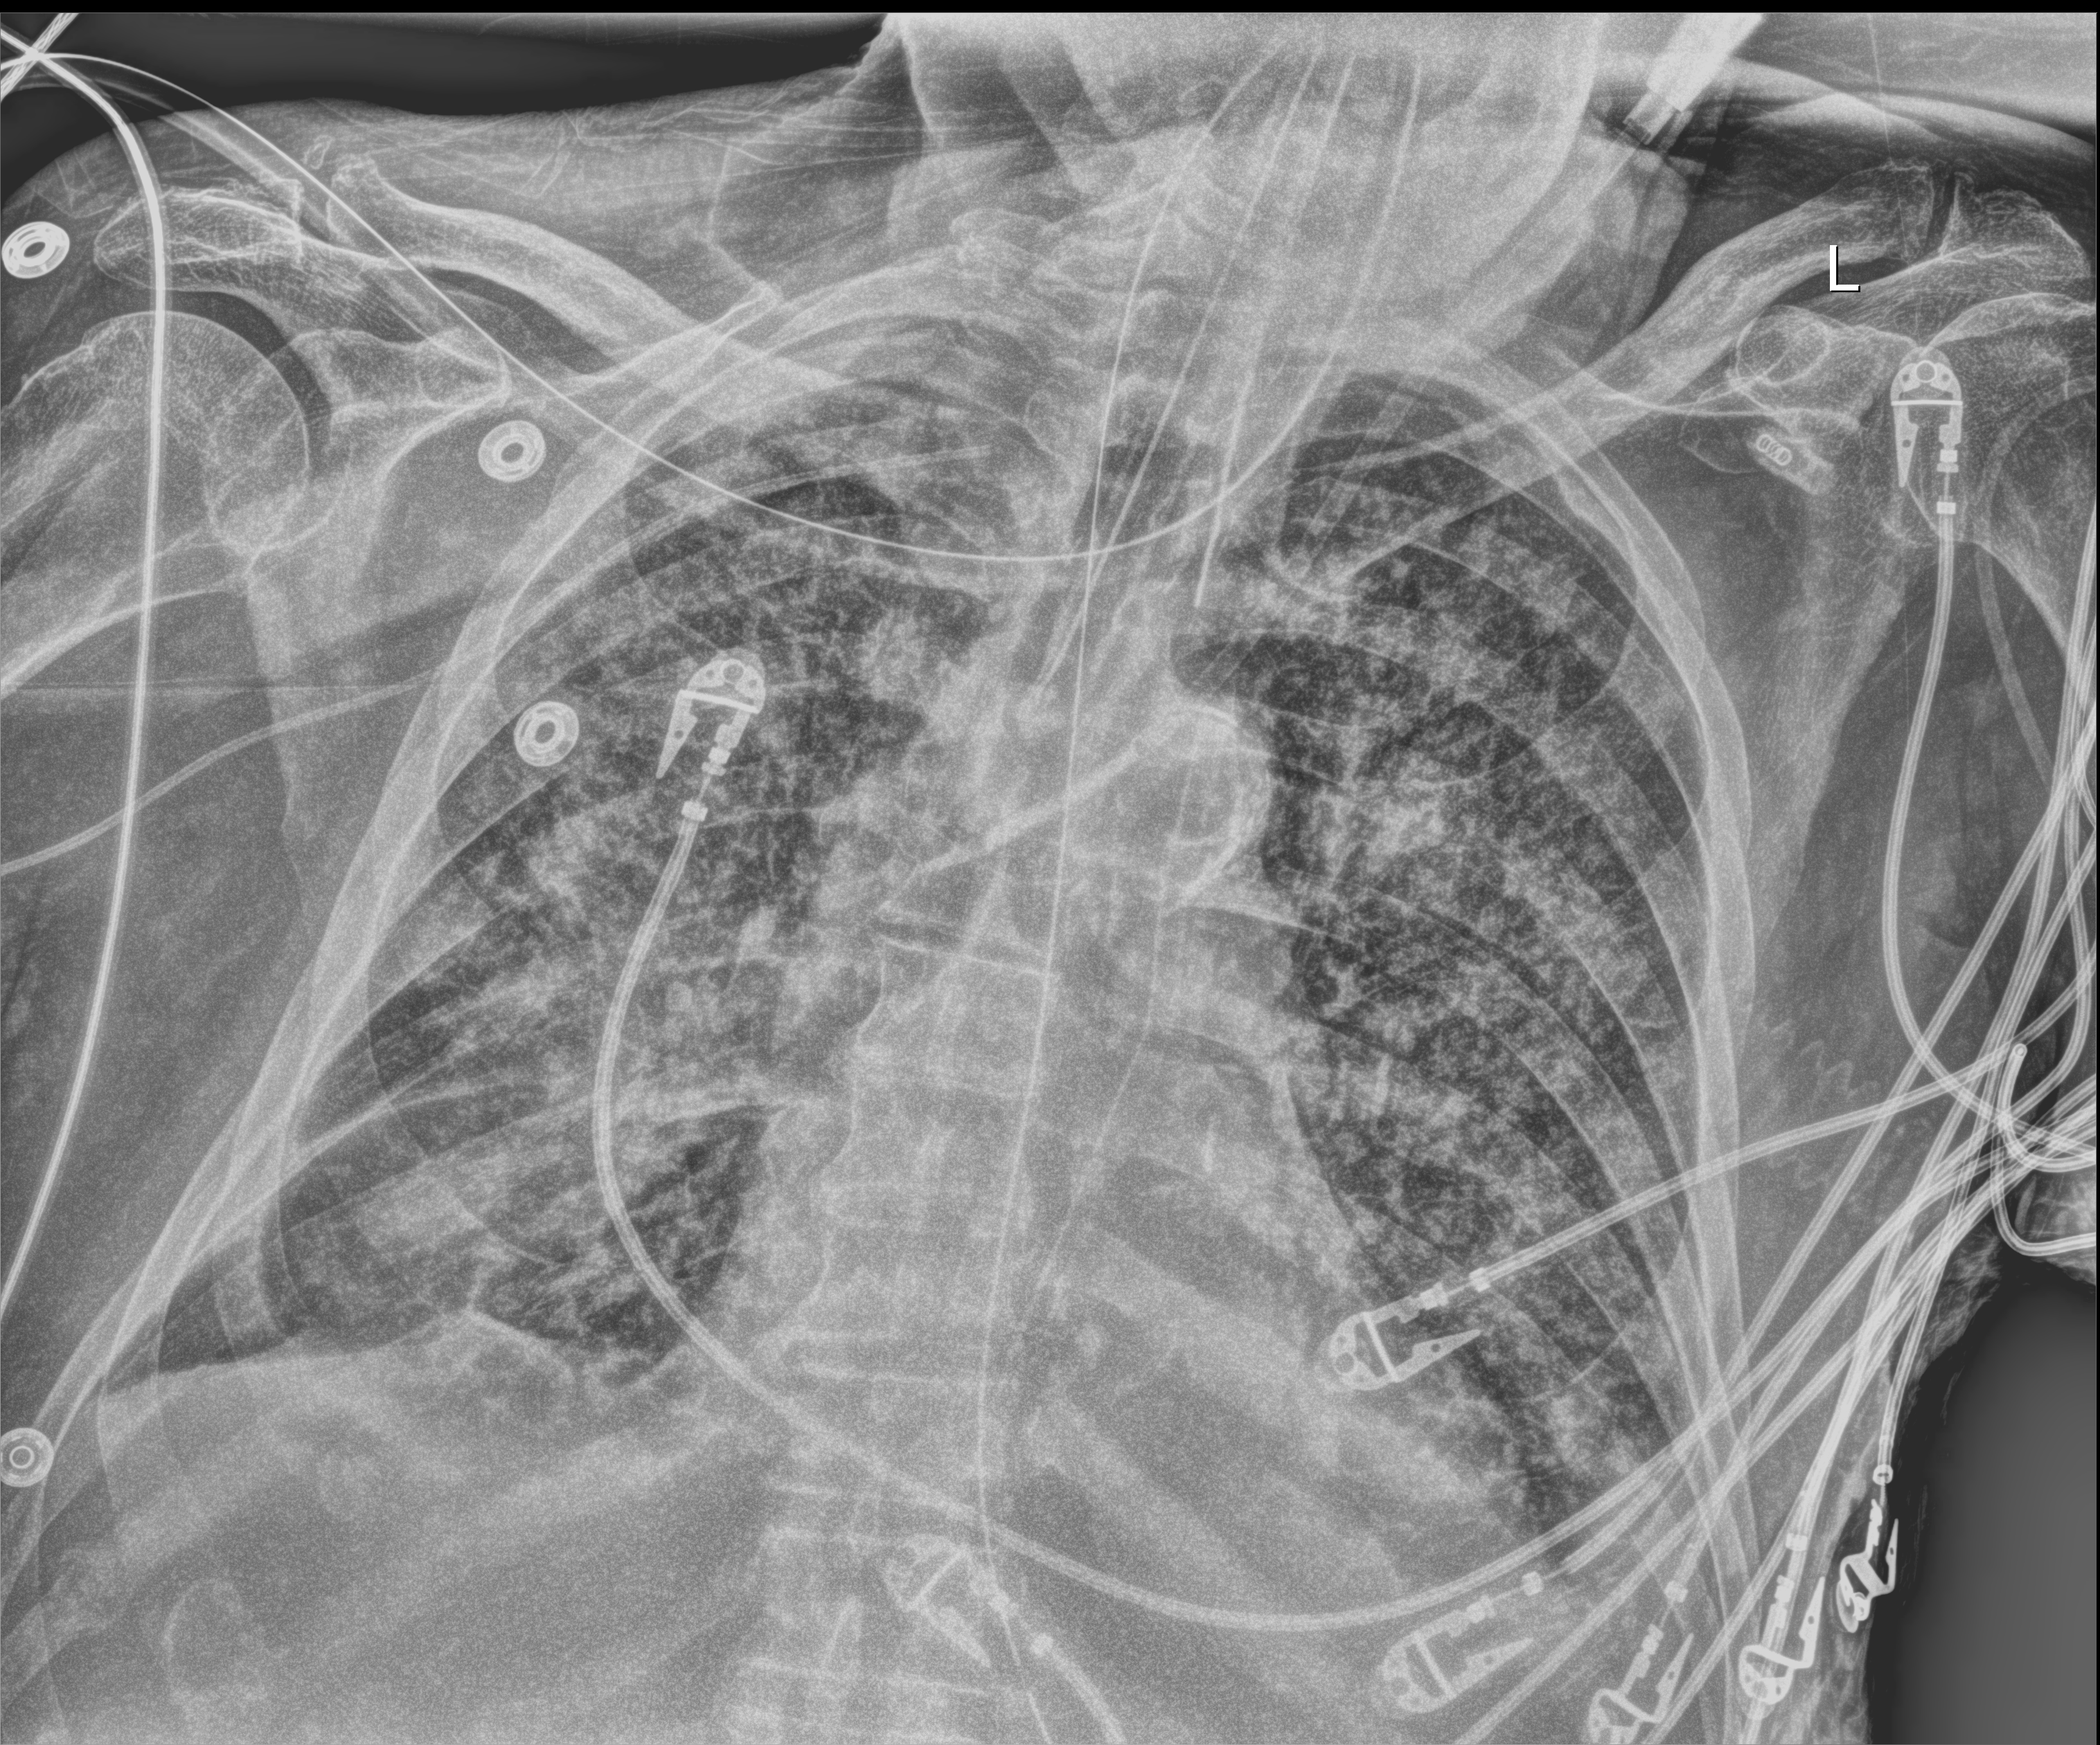
Bedside chest radiograph (digital radiography); anteroposterior (AP) projection. Patient hospitalised with COVID-19; male, aged 75–90 years.
Admission-level facts for this patient (not findings on this image; timing relative to this image not recorded):
- mechanically ventilated during this hospital stay: yes
- admitted to intensive care during this hospital stay: yes
- length of hospital stay: 28 days